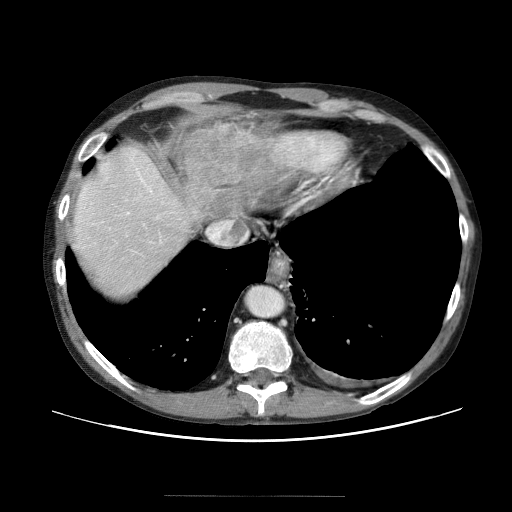
Contrast-enhanced abdominal CT (liver protocol), one axial slice. Position 55 of 69 along the scan axis. Reconstruction kernel STANDARD. Soft-tissue window (W 400 / L 40 HU). 512 × 512 image matrix, field of view 380 × 380 mm. Case-level facts recorded for this patient, not image findings: diagnosis: hepatocellular carcinoma (patient treated with transarterial chemoembolisation; whether this scan precedes or follows treatment is not stated here); TNM stage (as recorded): Stage-IVB; Child-Pugh class: B.
Outlined on this slice (semi-automatically segmented with operator editing):
- liver parenchyma outside the tumour (the mass and vessels are separate outlines, so this box may not span the whole liver): box from (x=66, y=116) to (x=322, y=316) px
- liver vessels: (x=119, y=201)–(x=152, y=243)